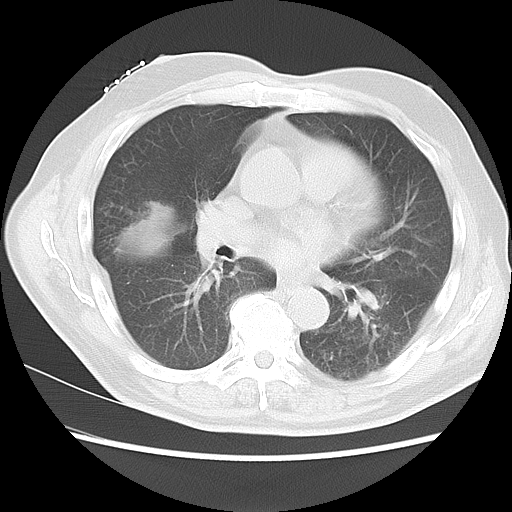
Chest CT, one axial slice; position 3 of 15 along the scan axis; reconstruction kernel LUNG; lung window (W 1500 / L -600 HU); 5 mm slice thickness; 512 × 512 image matrix, field of view 350 × 350 mm. Patient: male, 68 years. From the clinical record (not read from this slice): clinical TNM (as recorded): T4 N3 M0.
Structures marked on this image (rectangle marked by the reading radiologist):
- lung tumour (recorded histology: squamous cell carcinoma): box from (x=115, y=185) to (x=178, y=270) px